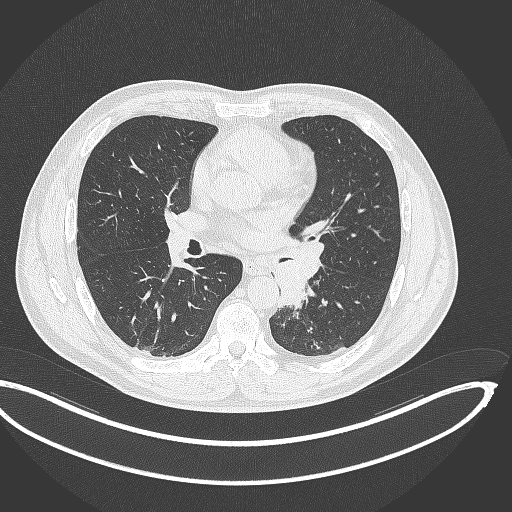
Chest CT, one axial slice. Position 185 of 362 along the scan axis. Reconstruction kernel B70f. 120 kVp. Lung window (W 1500 / L -600 HU). 1 mm slice thickness. 512 × 512 image matrix. Patient: male, 50 years. Case-level facts recorded for this patient, not image findings: clinical TNM (as recorded): T2a N3 M0.
Outlined on this slice (bounding box drawn by a radiologist):
- lung tumour (recorded histology: squamous cell carcinoma): bounding box <270,239,325,309> (left, top, right, bottom; pixels)